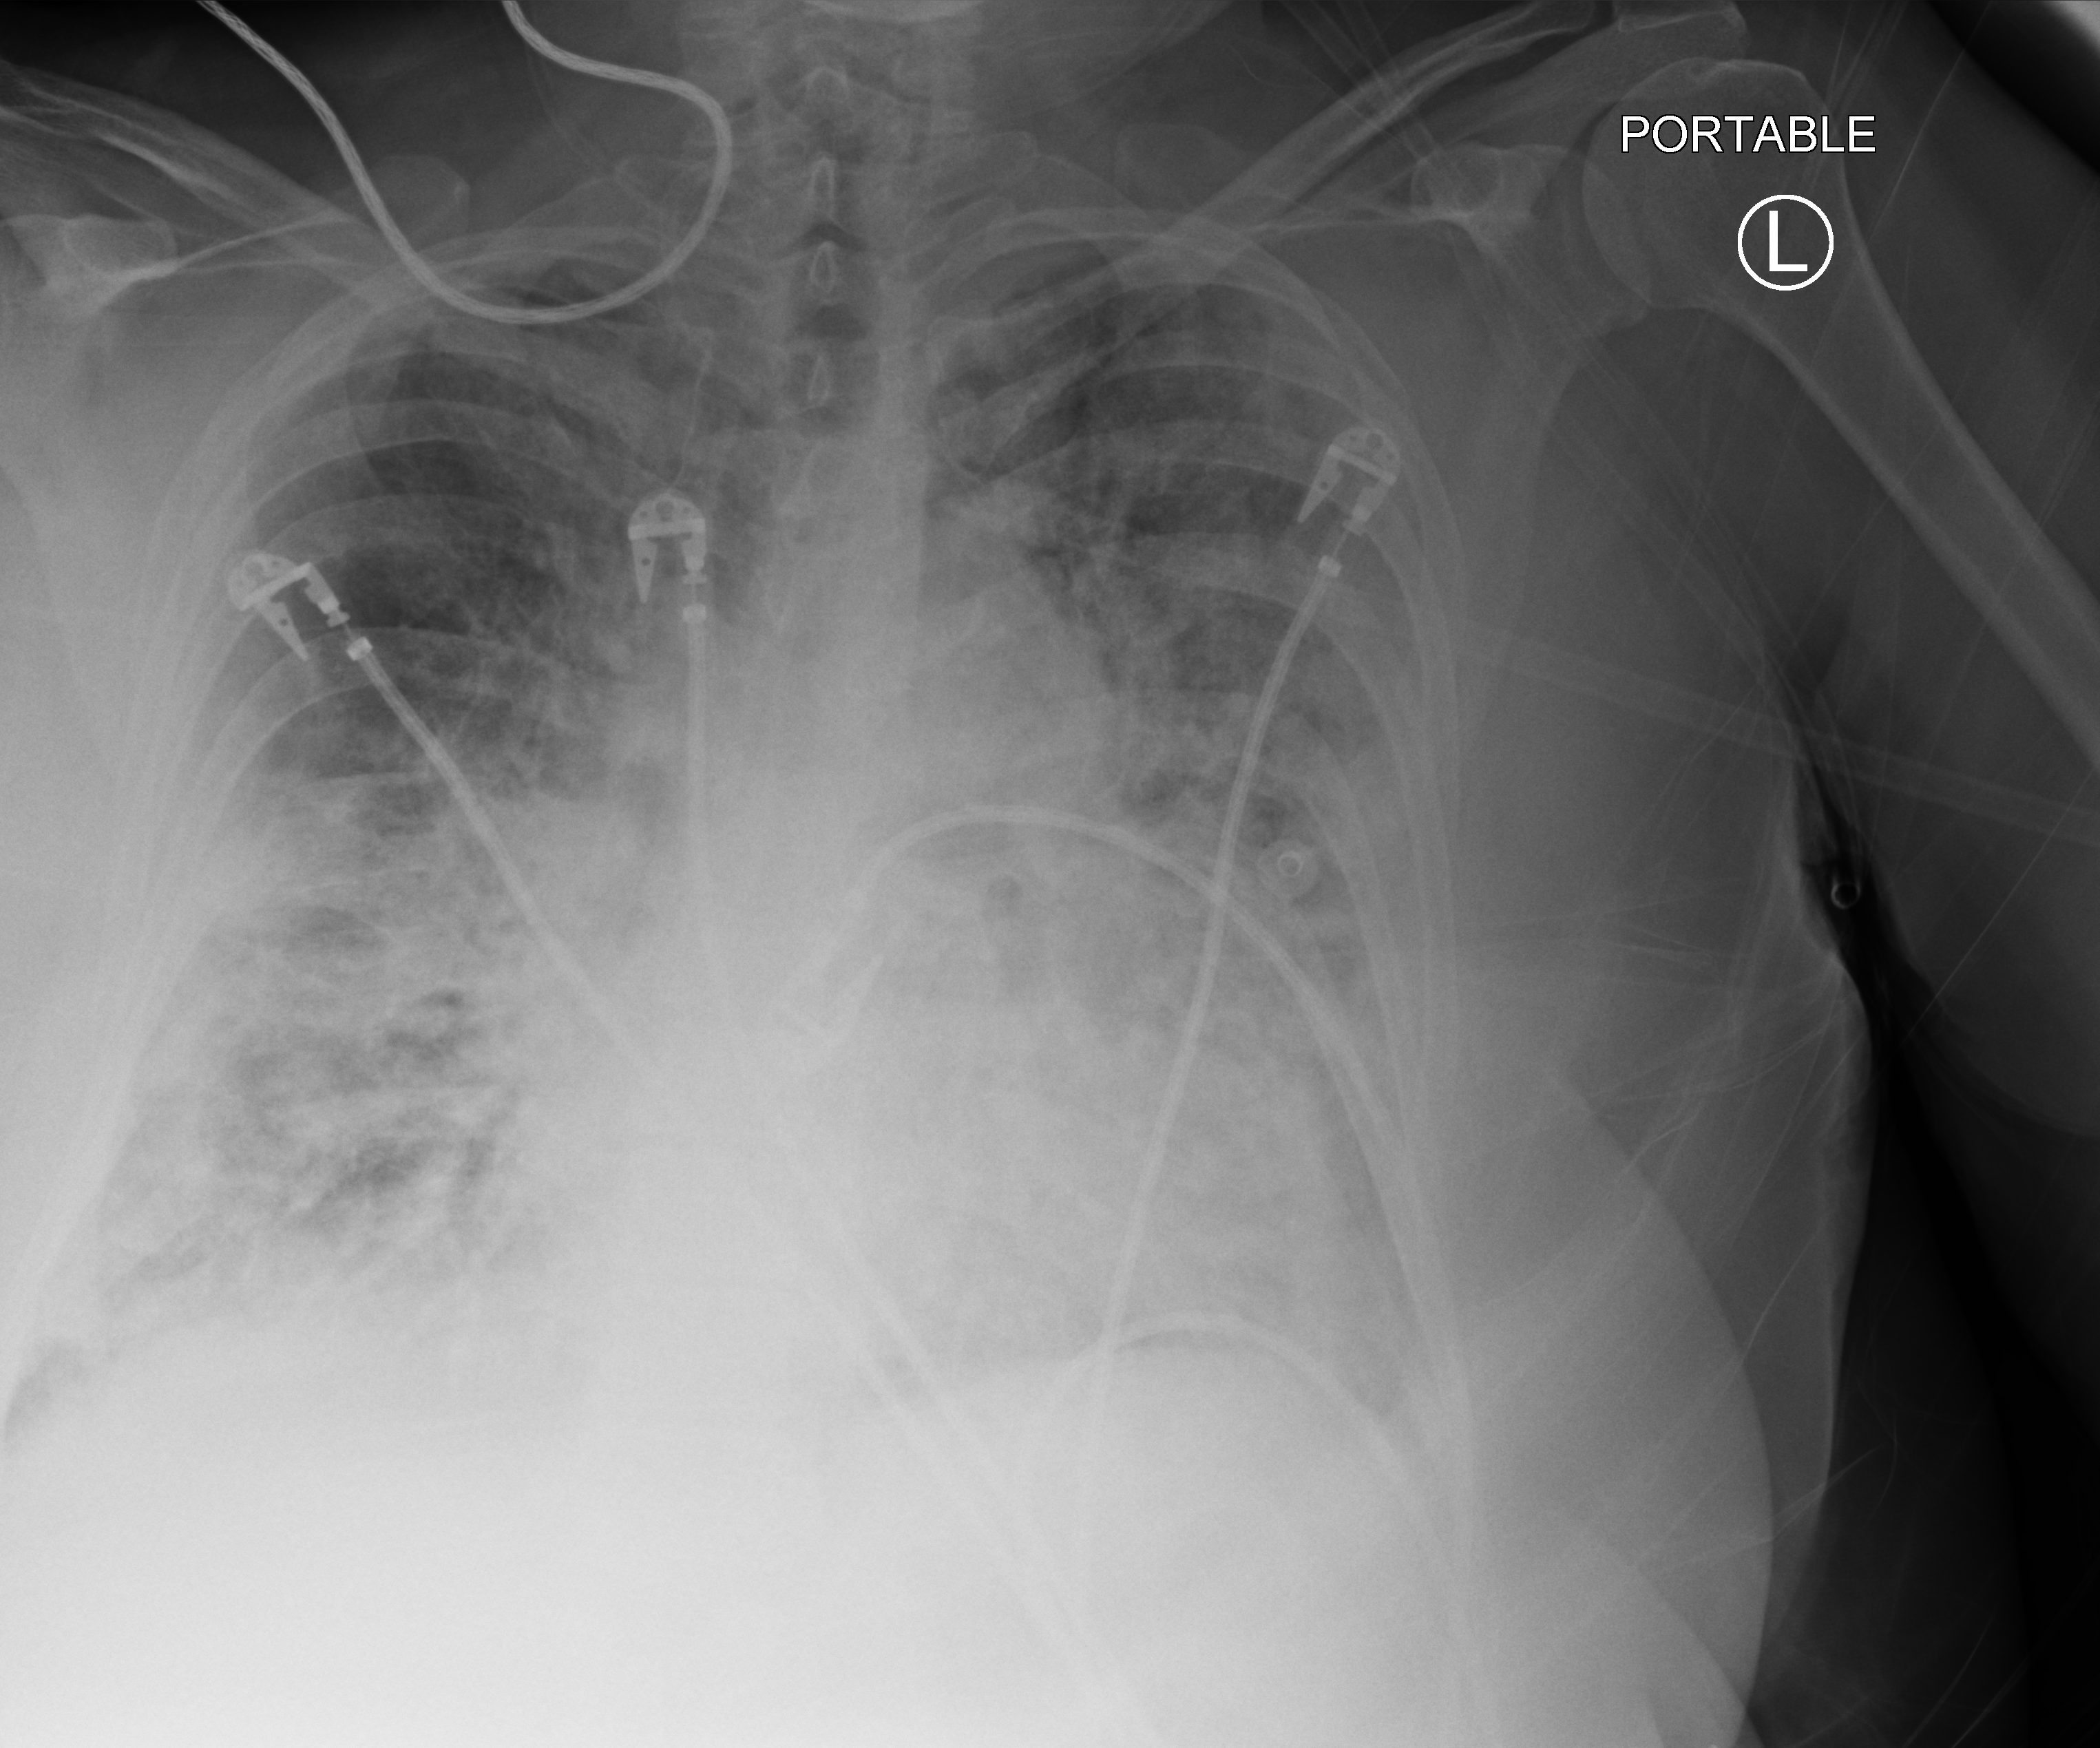
Chest X-ray (portable); anteroposterior (AP) projection. Female patient hospitalised with COVID-19, age 60–74 years.
Admission-level facts for this patient (not findings on this image; timing relative to this image not recorded): diabetes (admission record): no.